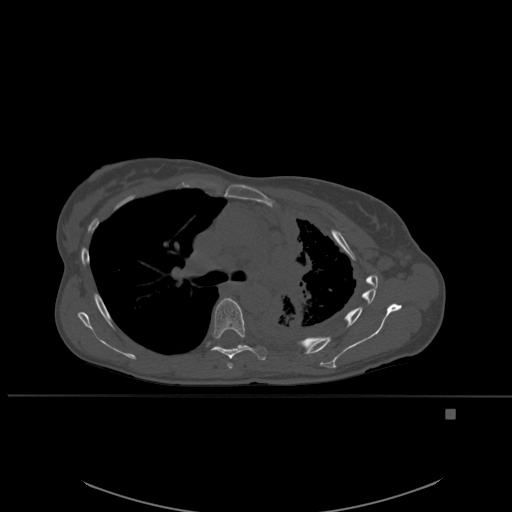
CT including the spine, one axial slice. Slice 383 of 537 in the series (ordered by position). Bone window (W 1800 / L 400 HU). 512 × 512 image matrix. Patient: female, 45 years. Case-level facts recorded for this patient, not image findings: primary cancer: lung.
Annotated regions visible in this slice (semi-automatic segmentation, software-assisted and operator-edited):
- T5 vertebra: bounding box <227,362,233,369> (left, top, right, bottom; pixels)
- T6 vertebra: <211,298,267,362>
- T7 vertebra: <220,344,244,348>